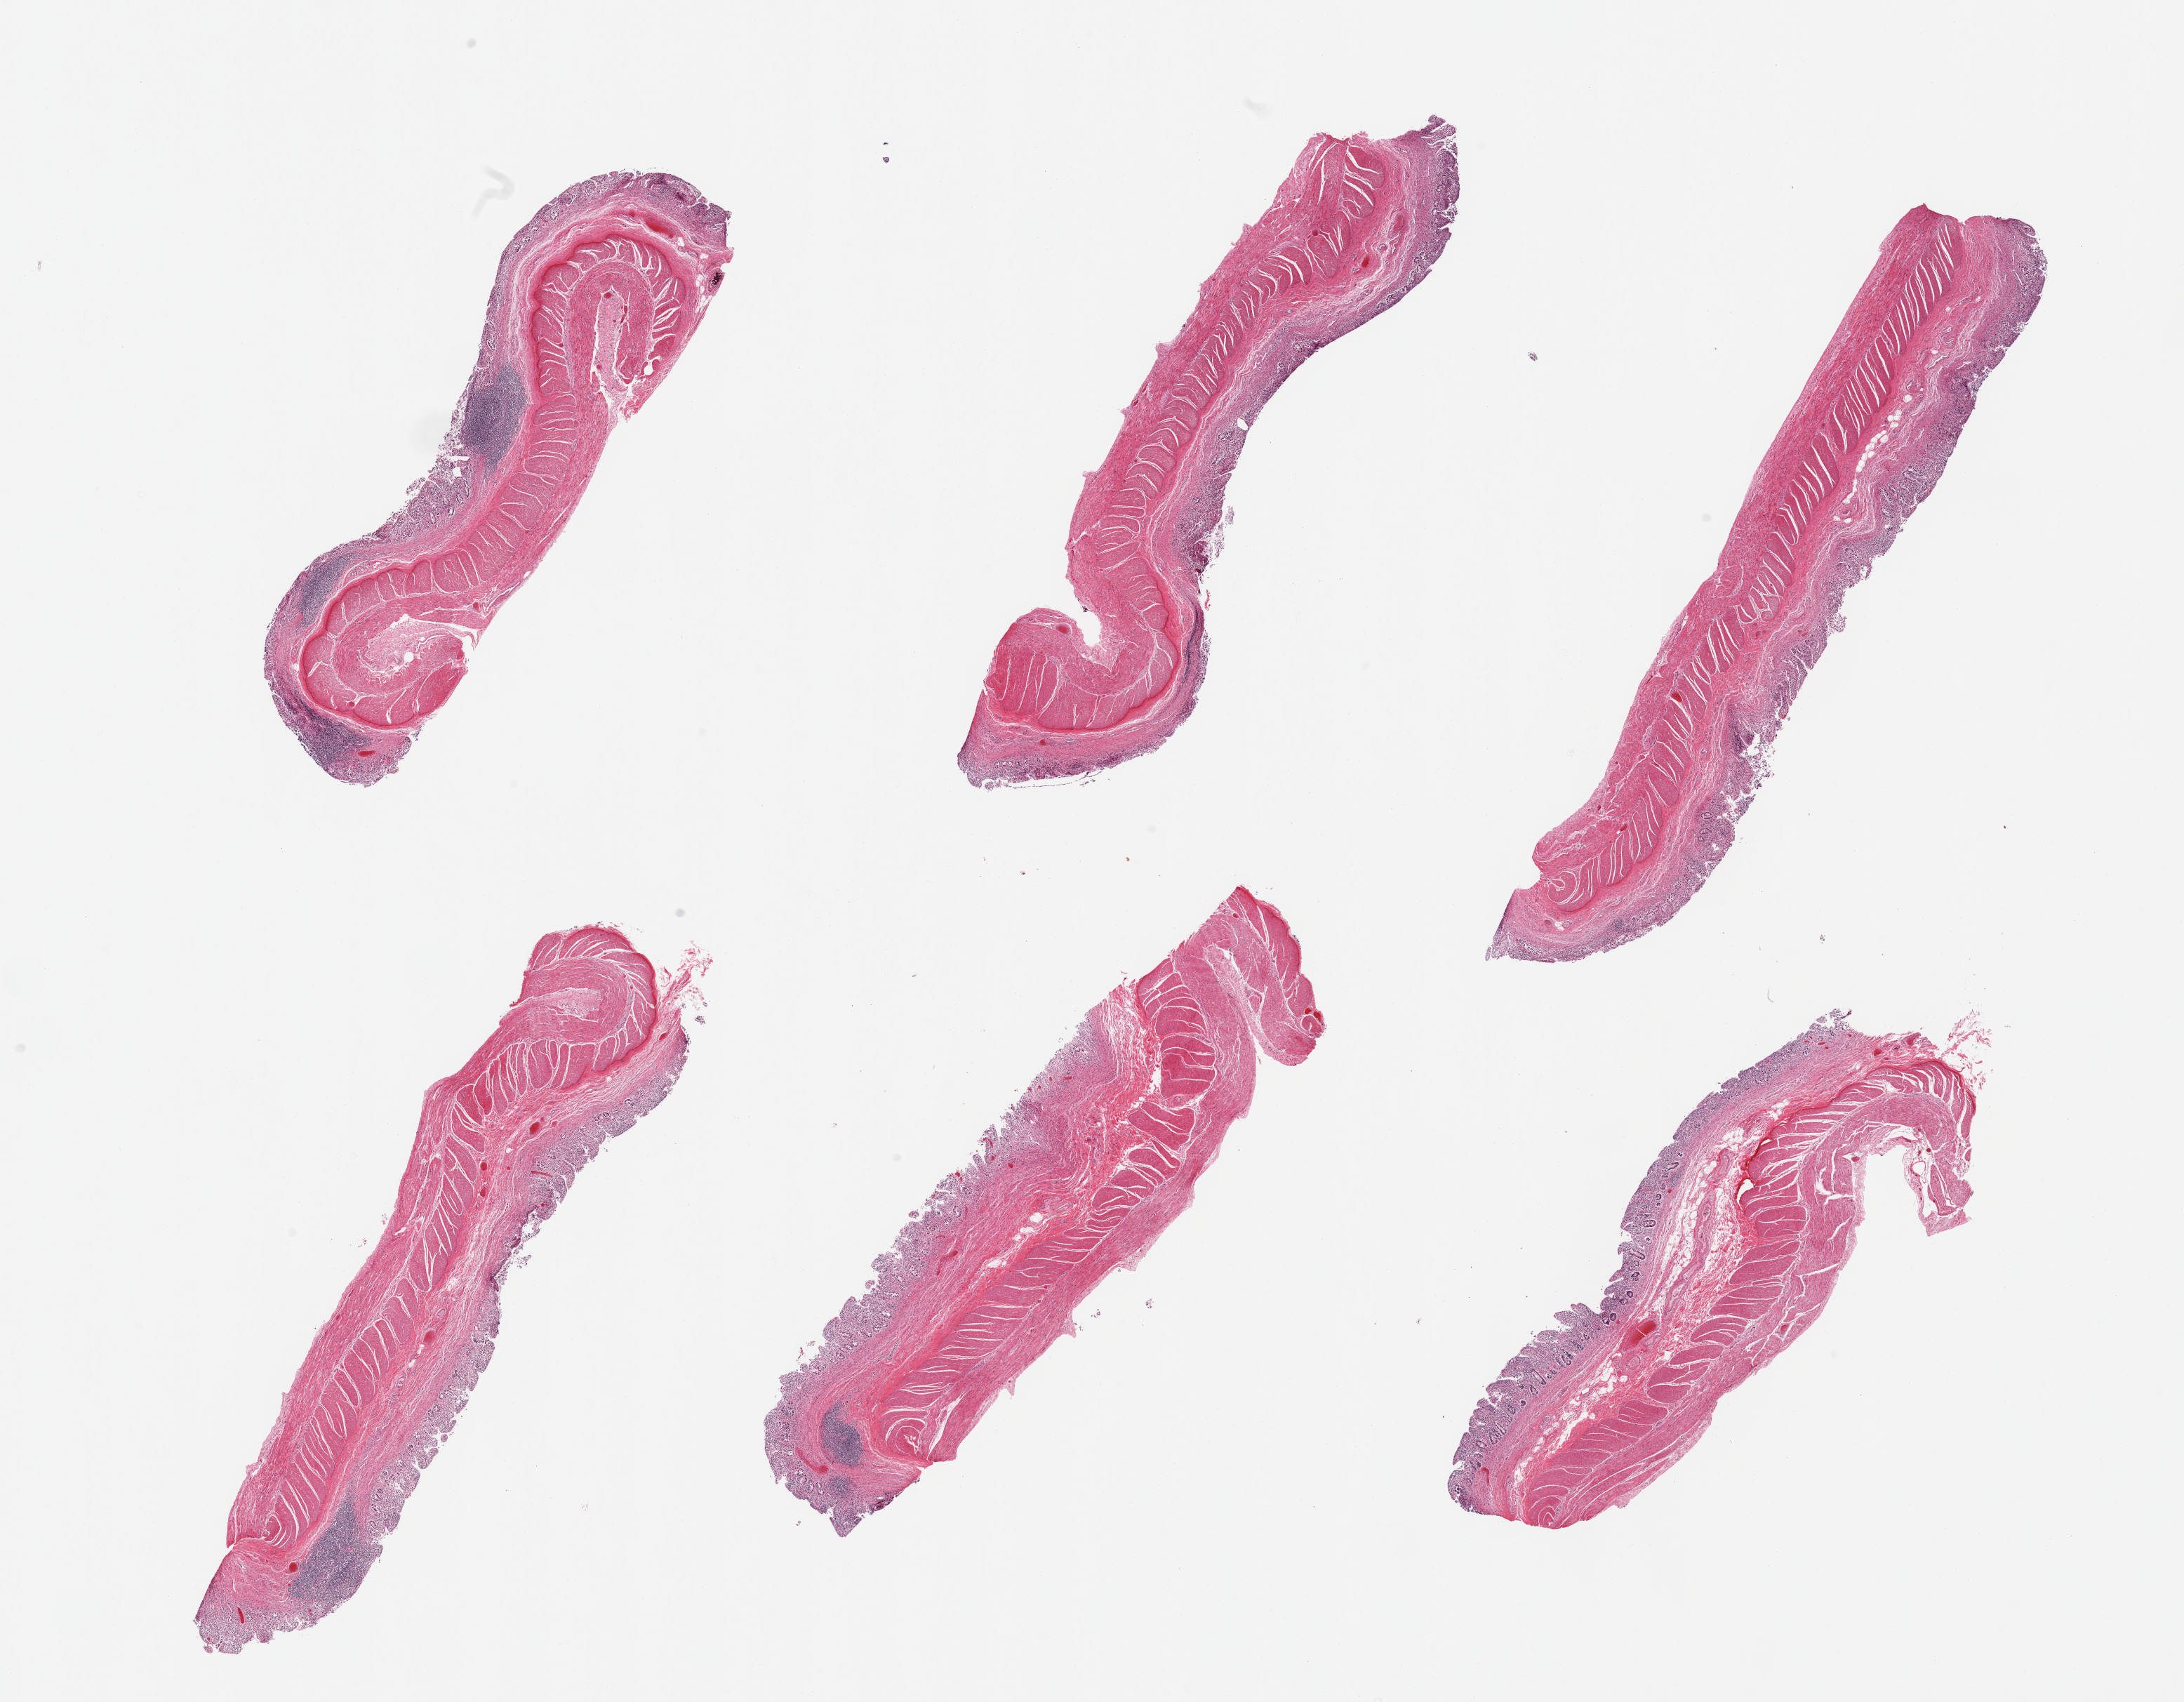
Haematoxylin and eosin whole-slide image — whole scanned area (about 24.6 x 19.2 mm, from a 20x scan) shown as a low-resolution overview; PAXgene-fixed, paraffin-embedded tissue; target tissue: transverse colon; donor tissue sample. Donor: female.
Reviewer comment on this tissue sample: 6 pieces; full thickness, mucosa autolyzed.